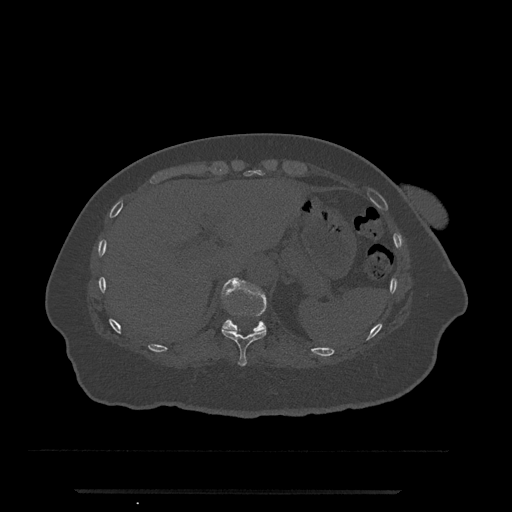
CT including the spine, one axial slice; position 263 of 797 along the scan axis; 120 kVp; bone window (W 1800 / L 400 HU); 0.5 mm slice thickness; 512 × 512 image matrix, field of view 440 × 440 mm. Female patient, age 51 years. Case-level facts recorded for this patient, not image findings: primary cancer: neuro; vertebrae with lytic lesions (as recorded): T8.
Outlined on this slice (semi-automatically segmented with operator editing):
- T10 vertebra: box from (x=221, y=327) to (x=267, y=366) px
- T11 vertebra: (x=223, y=278)–(x=267, y=332)